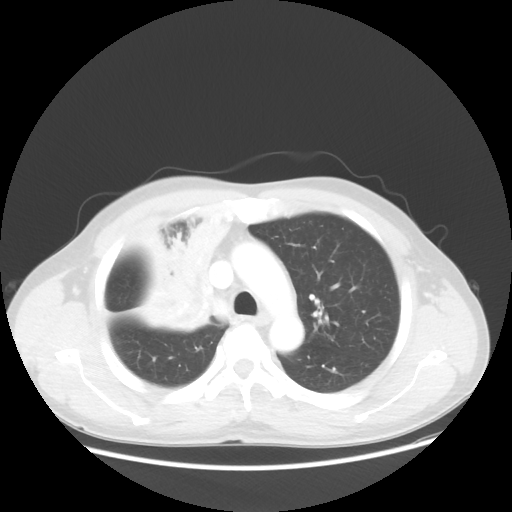
Chest CT, one axial slice. Position 39 of 56 along the scan axis. Lung window (W 1500 / L -600 HU). 5 mm slice thickness. 512 × 512 image matrix, field of view 398 × 398 mm. Patient: male, 60 years. Case-level facts recorded for this patient, not image findings: clinical TNM (as recorded): T2a N1 M0.
Outlined on this slice (rectangle marked by the reading radiologist):
- lung tumour (recorded histology: squamous cell carcinoma): bounding box [x1, y1, x2, y2] px = [132, 208, 238, 348]